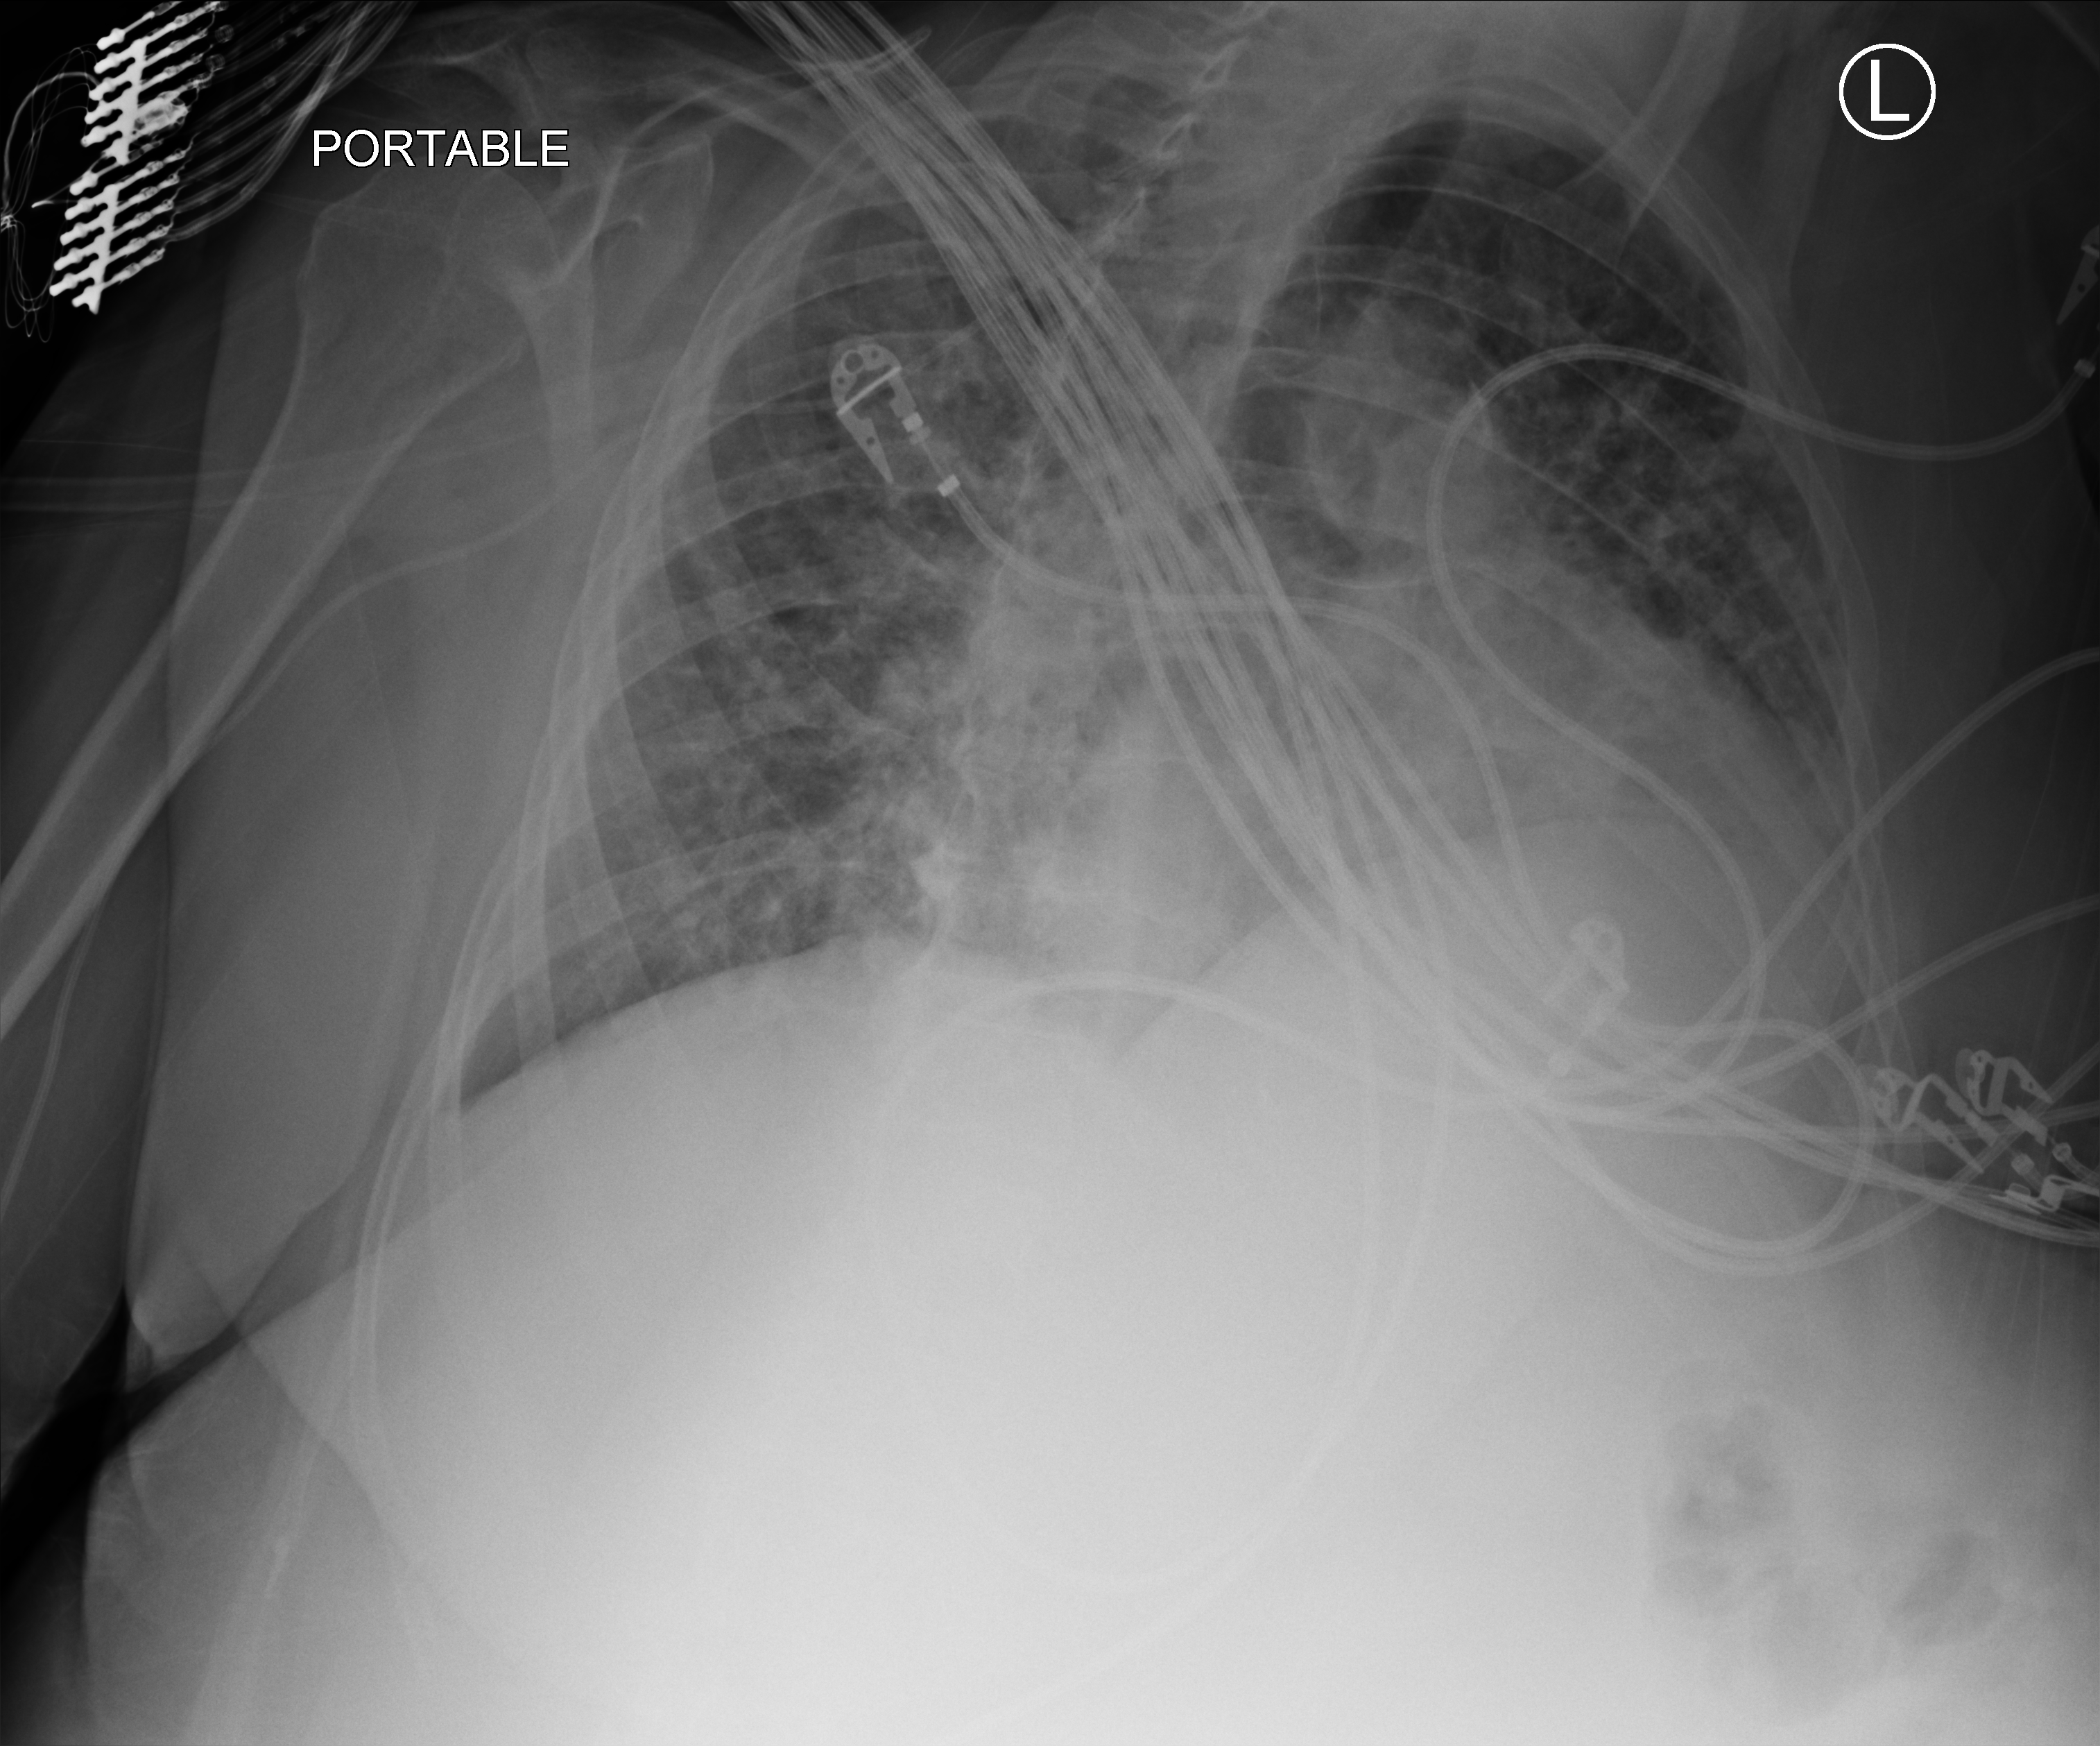
Portable chest radiograph; anteroposterior (AP) projection. Patient hospitalised with COVID-19; female, aged 75–90 years.
Admission-level facts for this patient (not findings on this image; timing relative to this image not recorded): admitted to intensive care during this hospital stay: yes; mechanically ventilated during this hospital stay: yes; hypertension (admission record): yes.